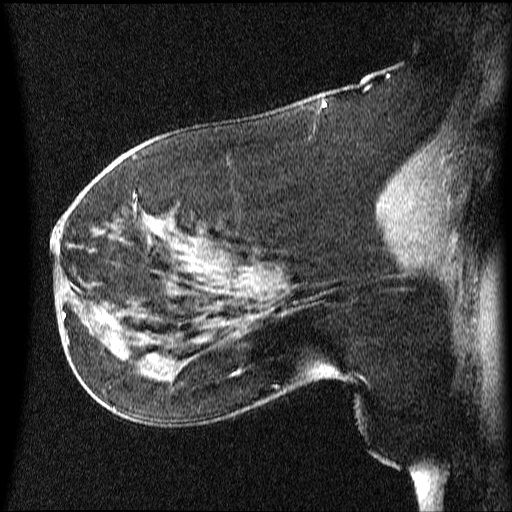
Breast MRI (dynamic contrast-enhanced), one sagittal slice. Position 34 of 64 along the scan axis. Dynamic contrast-enhanced series, image 2 of 4 at this slice position (ordered by acquisition). 1.5 T. TE 4.2 ms, TR 9 ms. 512 × 512 image matrix, field of view 200 × 200 mm. Female patient, age 63 years.
Structures marked on this image (semi-automatically segmented with operator editing):
- analysis volume of interest (the breast-tissue region the enhancement analysis was run in; not a lesion): bounding box <66,280,131,353> (left, top, right, bottom; pixels)
- tumour enhancement mask (voxels above the 70 % enhancement threshold inside the analysis volume of interest): <99,318,126,353>